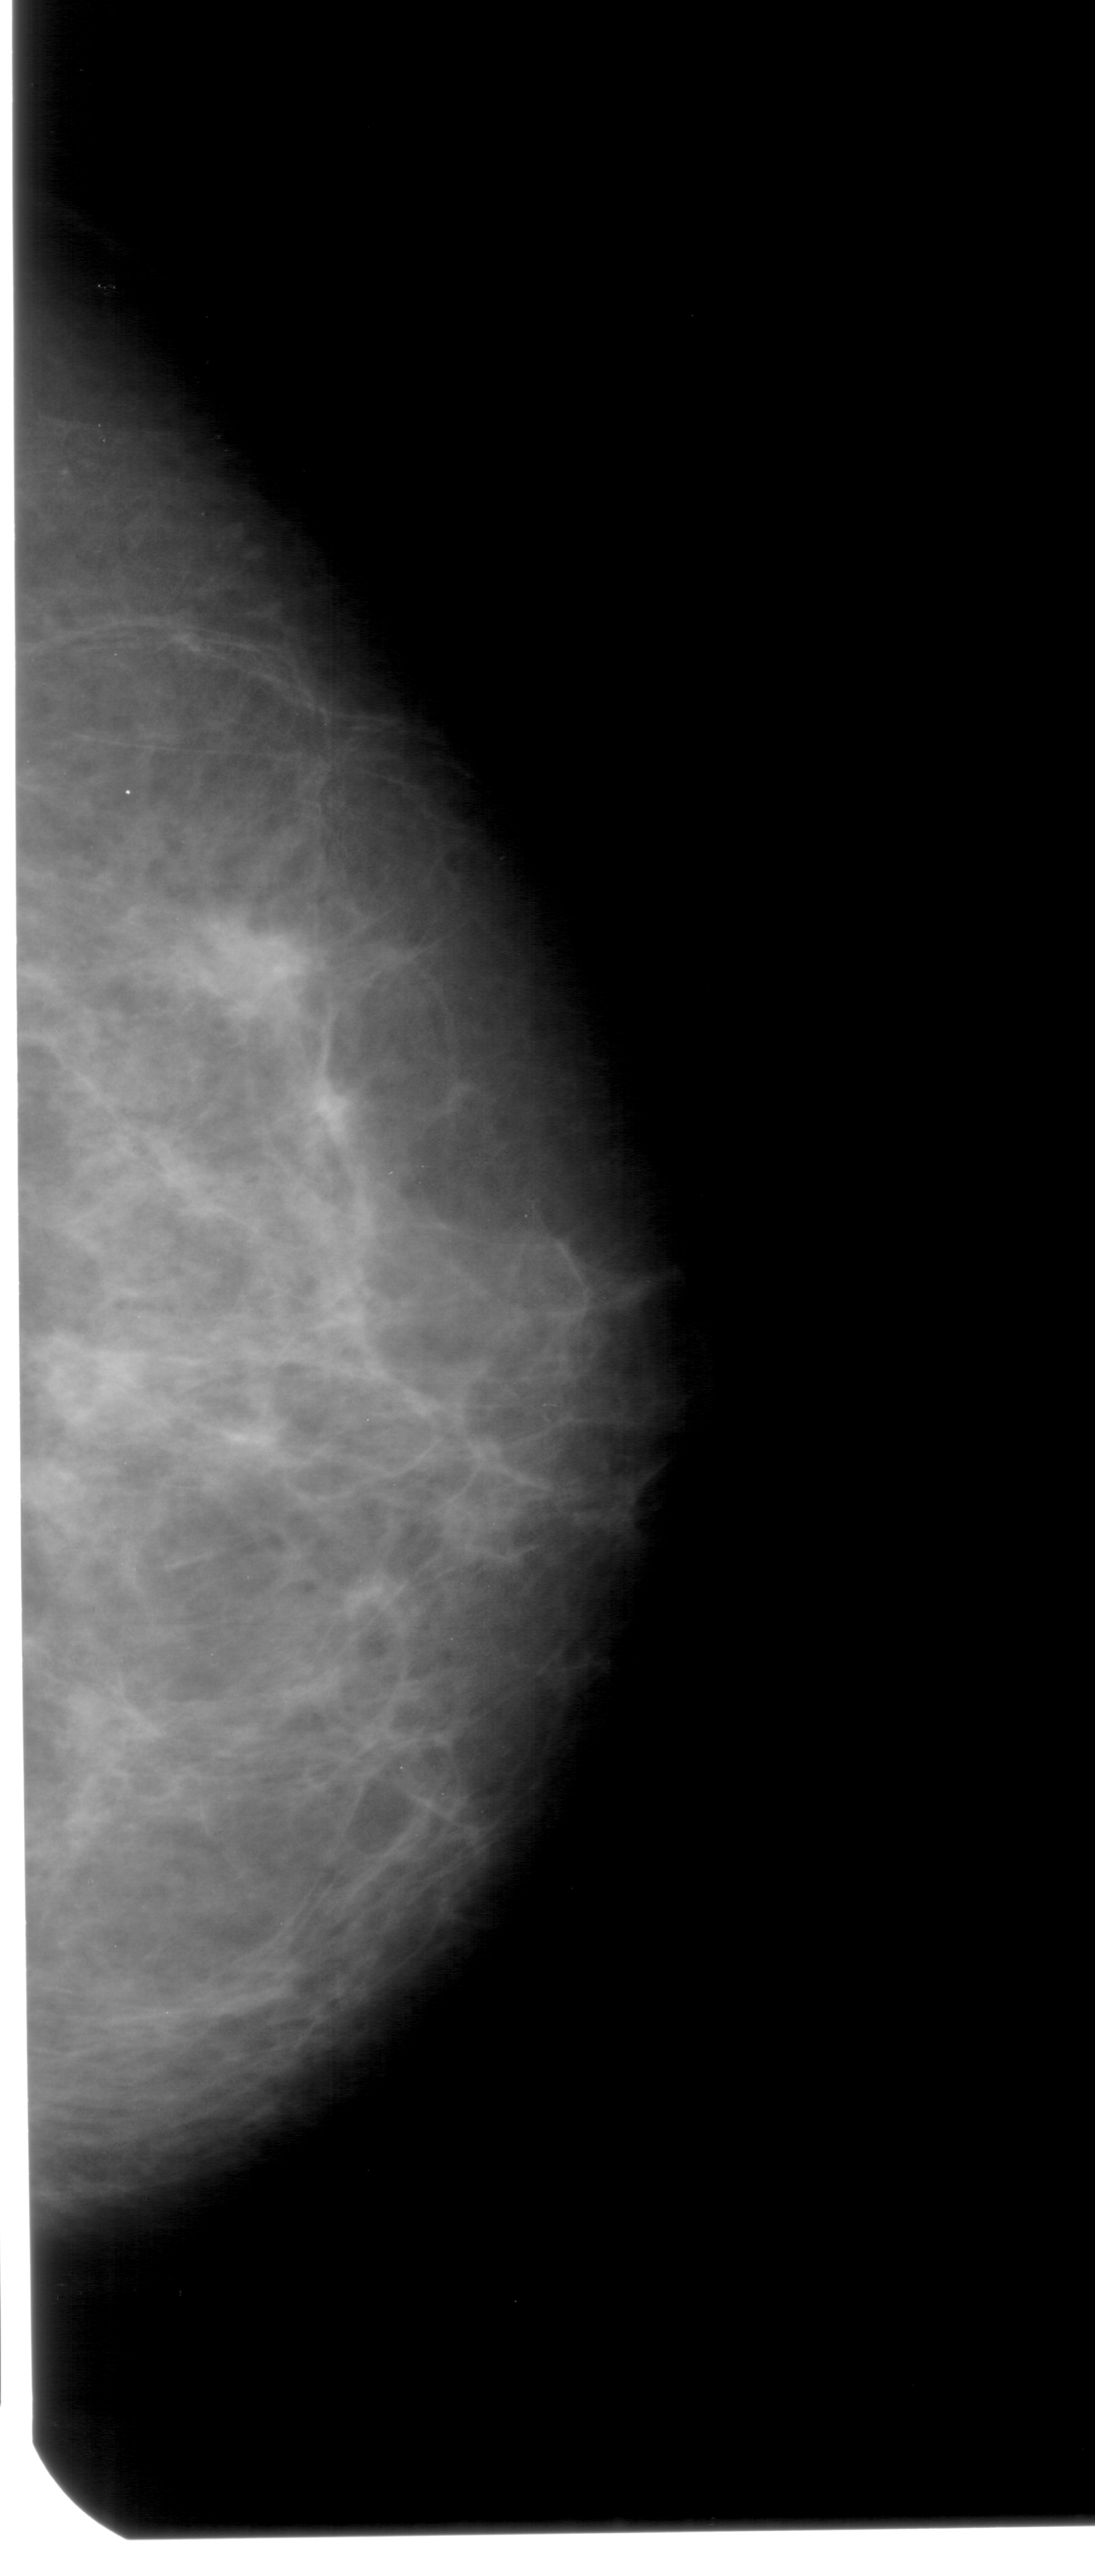
Mammogram (digitized film), right breast, craniocaudal (CC) view.
Marked abnormality: mass, shape focal asymmetric density, margins ill defined; BI-RADS assessment category 4; subtlety rating 1 on a 1 (subtle) to 5 (obvious) scale; pathology result (as recorded, not read from the image): benign.